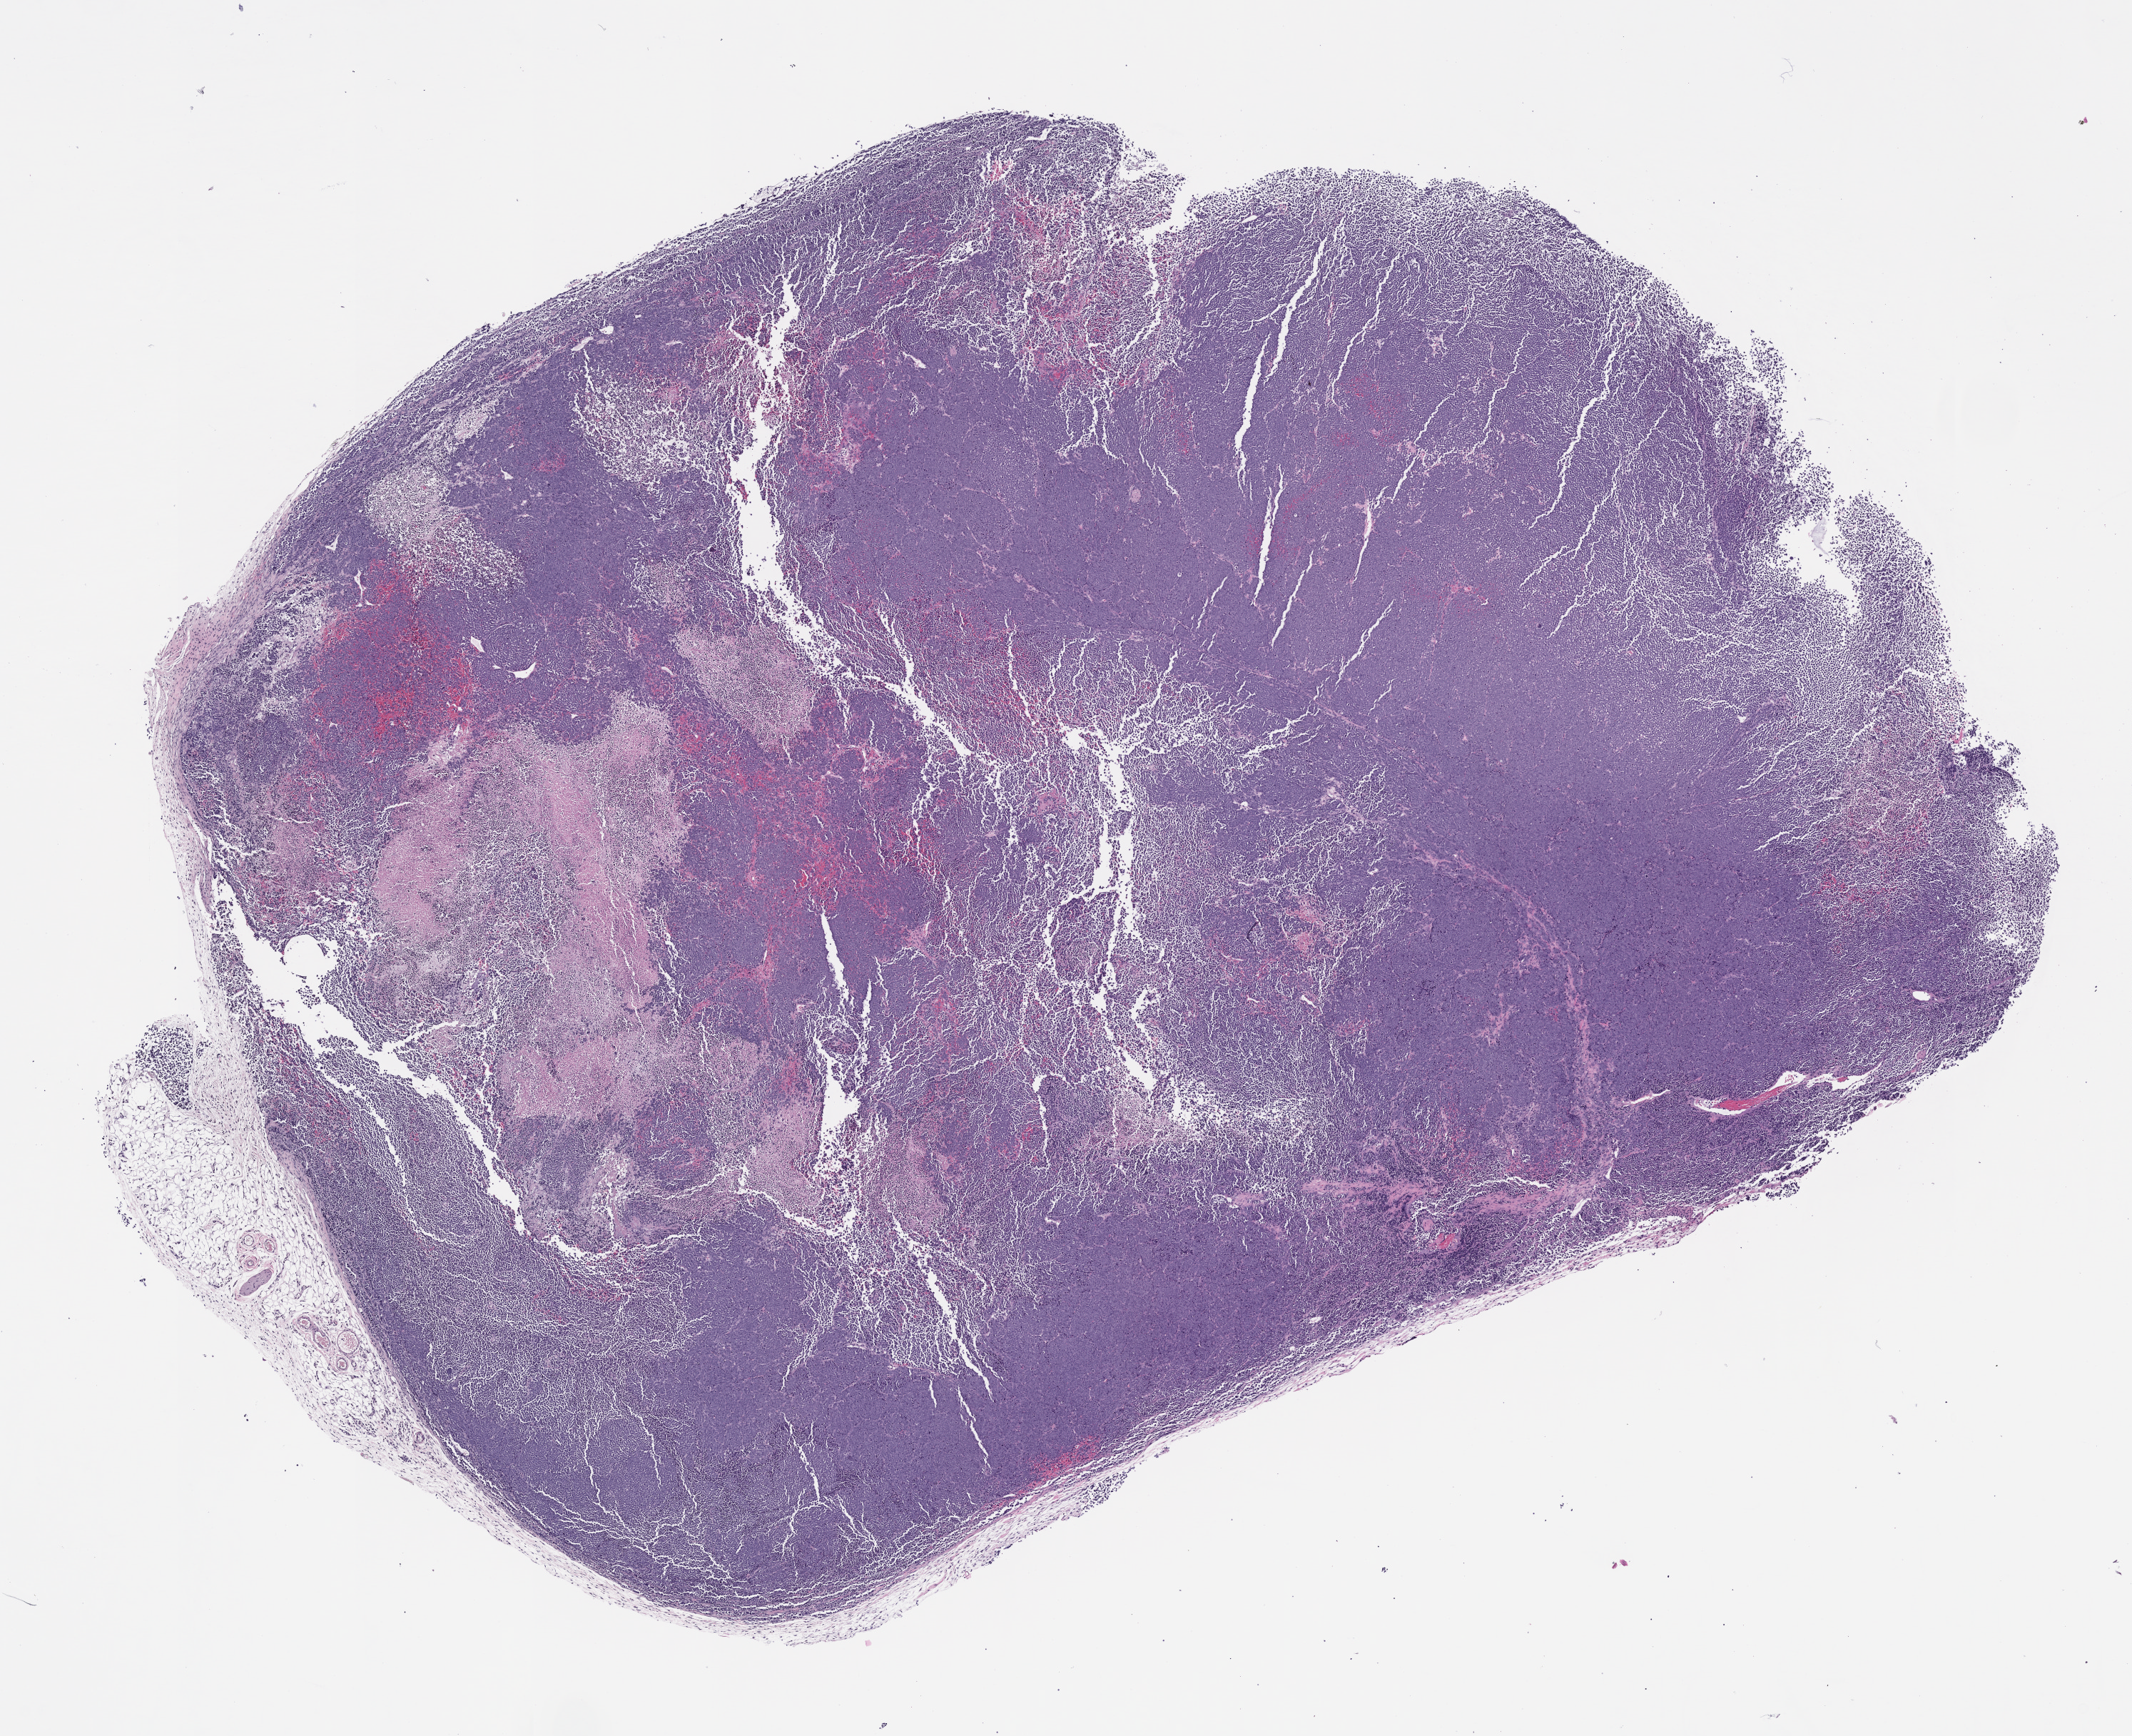
Whole-slide image, haematoxylin and eosin: patient-derived xenograft (human tumor grown in a mouse), passage 1, shown as a low-resolution overview of the whole scanned area (about 12.0 x 9.8 mm), formalin-fixed, paraffin-embedded (FFPE) tissue, tumor site category: endocrine.
Originating patient diagnosis: Merkel Cell Carcinoma.